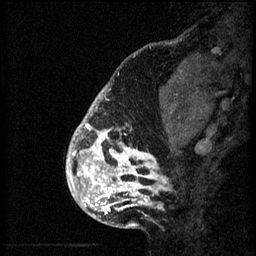
Breast MRI (dynamic contrast-enhanced), one sagittal slice. Slice 17 of 60 in the series (ordered by position). 3 images stored at this slice position (order not interpretable as contrast timing). 1.5 T. TE 4.2 ms, TR 8.2 ms. 2 mm slice thickness. 256 × 256 image matrix, field of view 180 × 180 mm. Patient: female, 41 years.
Outlined on this slice (semi-automatic segmentation, software-assisted and operator-edited):
- analysis volume of interest (the breast-tissue region the enhancement analysis was run in; not a lesion): bounding box <72,108,176,205> (left, top, right, bottom; pixels)
- tumour enhancement mask (voxels above the 70 % enhancement threshold inside the analysis volume of interest): <72,108,168,205>